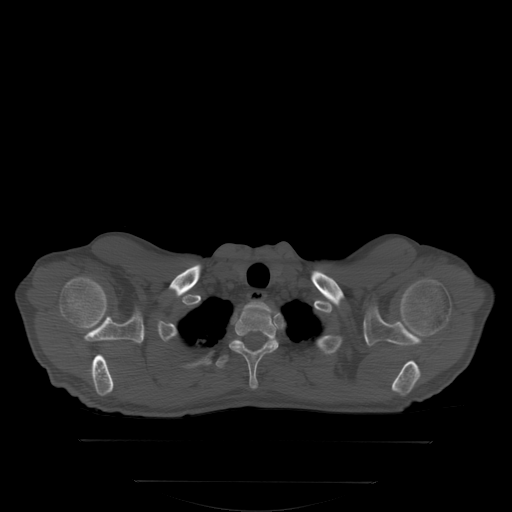
CT including the spine, one axial slice. Slice 286 of 350 in the series (ordered by position). Bone window (W 1800 / L 400 HU). 2.5 mm slice thickness. 512 × 512 image matrix, field of view 500 × 500 mm. Patient: male, 58 years. Case-level facts recorded for this patient, not image findings: primary cancer: prostate.
Outlined on this slice (semi-automatic segmentation, software-assisted and operator-edited):
- T1 vertebra: bounding box (x1, y1, x2, y2) in pixels: (225, 309, 278, 388)
- T2 vertebra: (219, 361, 225, 368)